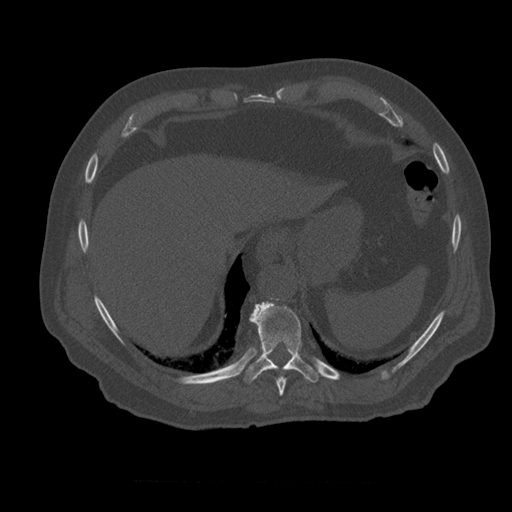
CT including the spine, one axial slice; slice 305 of 399 in the series (ordered by position); 120 kVp; bone window (W 1800 / L 400 HU); 512 × 512 image matrix, field of view 407 × 407 mm. Patient age 73 years. Case-level facts recorded for this patient, not image findings: primary cancer: prostate; vertebrae with lytic lesions (as recorded): L2.
Annotated regions visible in this slice (semi-automatic segmentation, software-assisted and operator-edited):
- T10 vertebra: bounding box [x1, y1, x2, y2] px = [243, 302, 321, 383]
- T9 vertebra: [275, 369, 287, 396]